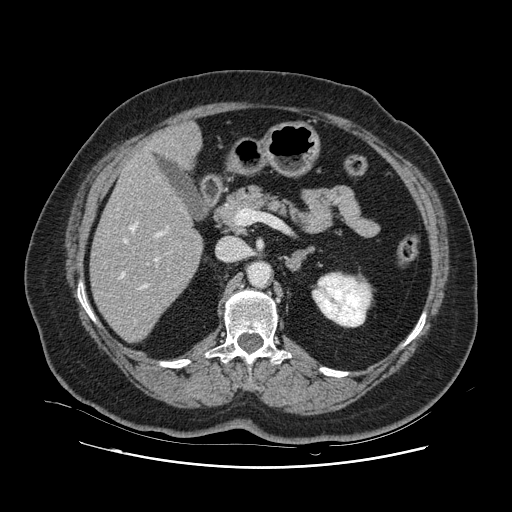
Contrast-enhanced abdominal CT, one axial slice; position 52 of 132 along the scan axis; intravenous contrast given; soft-tissue window (W 400 / L 40 HU); 512 × 512 image matrix, field of view 391 × 391 mm. Female patient, age 73 years. From the clinical record (not read from this slice): diagnosis: colorectal cancer liver metastases, imaged before liver resection.
Annotated regions visible in this slice (manually delineated by an expert):
- hepatic veins: bounding box (x1, y1, x2, y2) in pixels: (120, 176, 168, 321)
- liver: (91, 124, 203, 342)
- planned liver remnant (the part of the liver to remain after resection): (91, 147, 203, 342)
- portal vein (with intrahepatic branches): (138, 227, 169, 290)